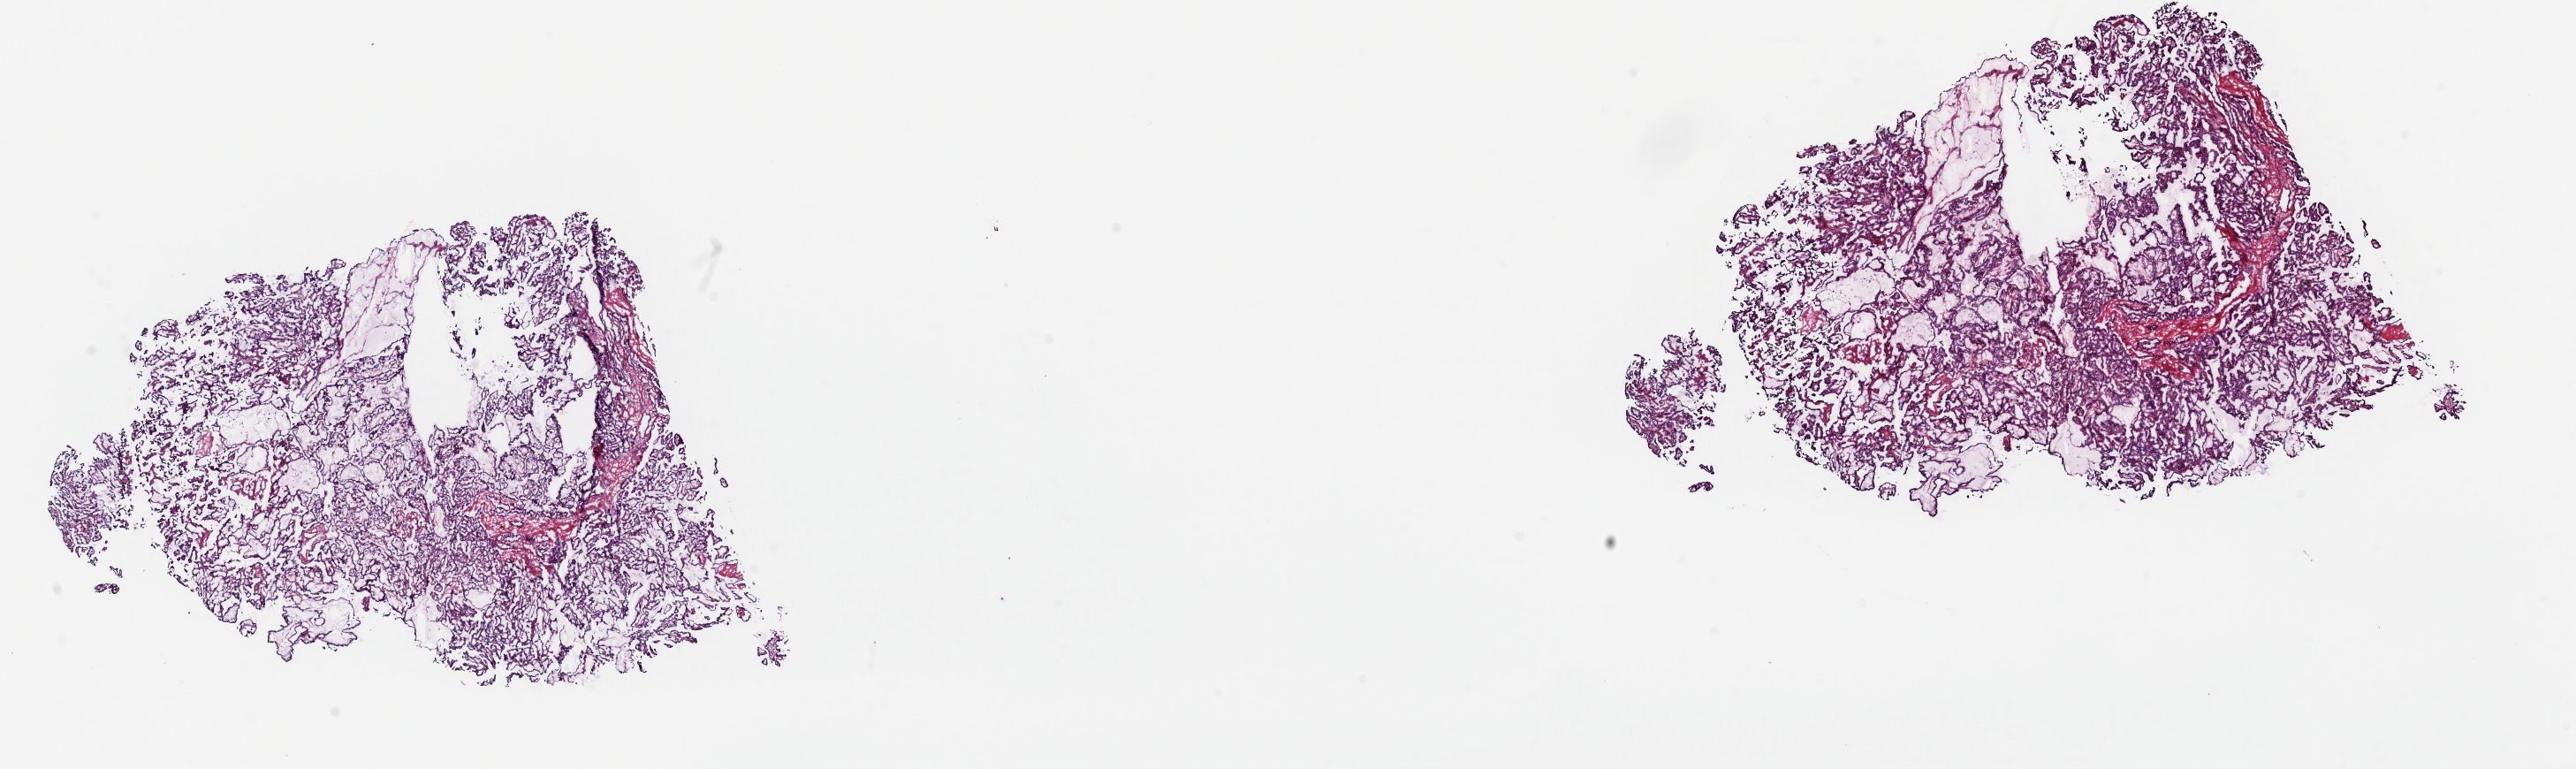
Digitized H&E tissue section (whole slide), a low-resolution overview of the entire scanned area, about 23.0 x 6.9 mm (acquisition: 40x scan), frozen section from the top of the tissue portion, sample: primary tumour, thyroid. Female, age 18 years at initial diagnosis. Pathologist review of this section (percent, as recorded): tumour cells 95%, tumour nuclei 90%, normal cells 0%, stromal cells 5%, necrosis 0%. Inflammatory infiltration, as recorded: lymphocyte infiltration 0%, monocyte infiltration 0%, neutrophil infiltration 0%.
Pathologic diagnosis: Papillary adenocarcinoma, NOS (thyroid gland). AJCC pathologic stage: I (6th edition).